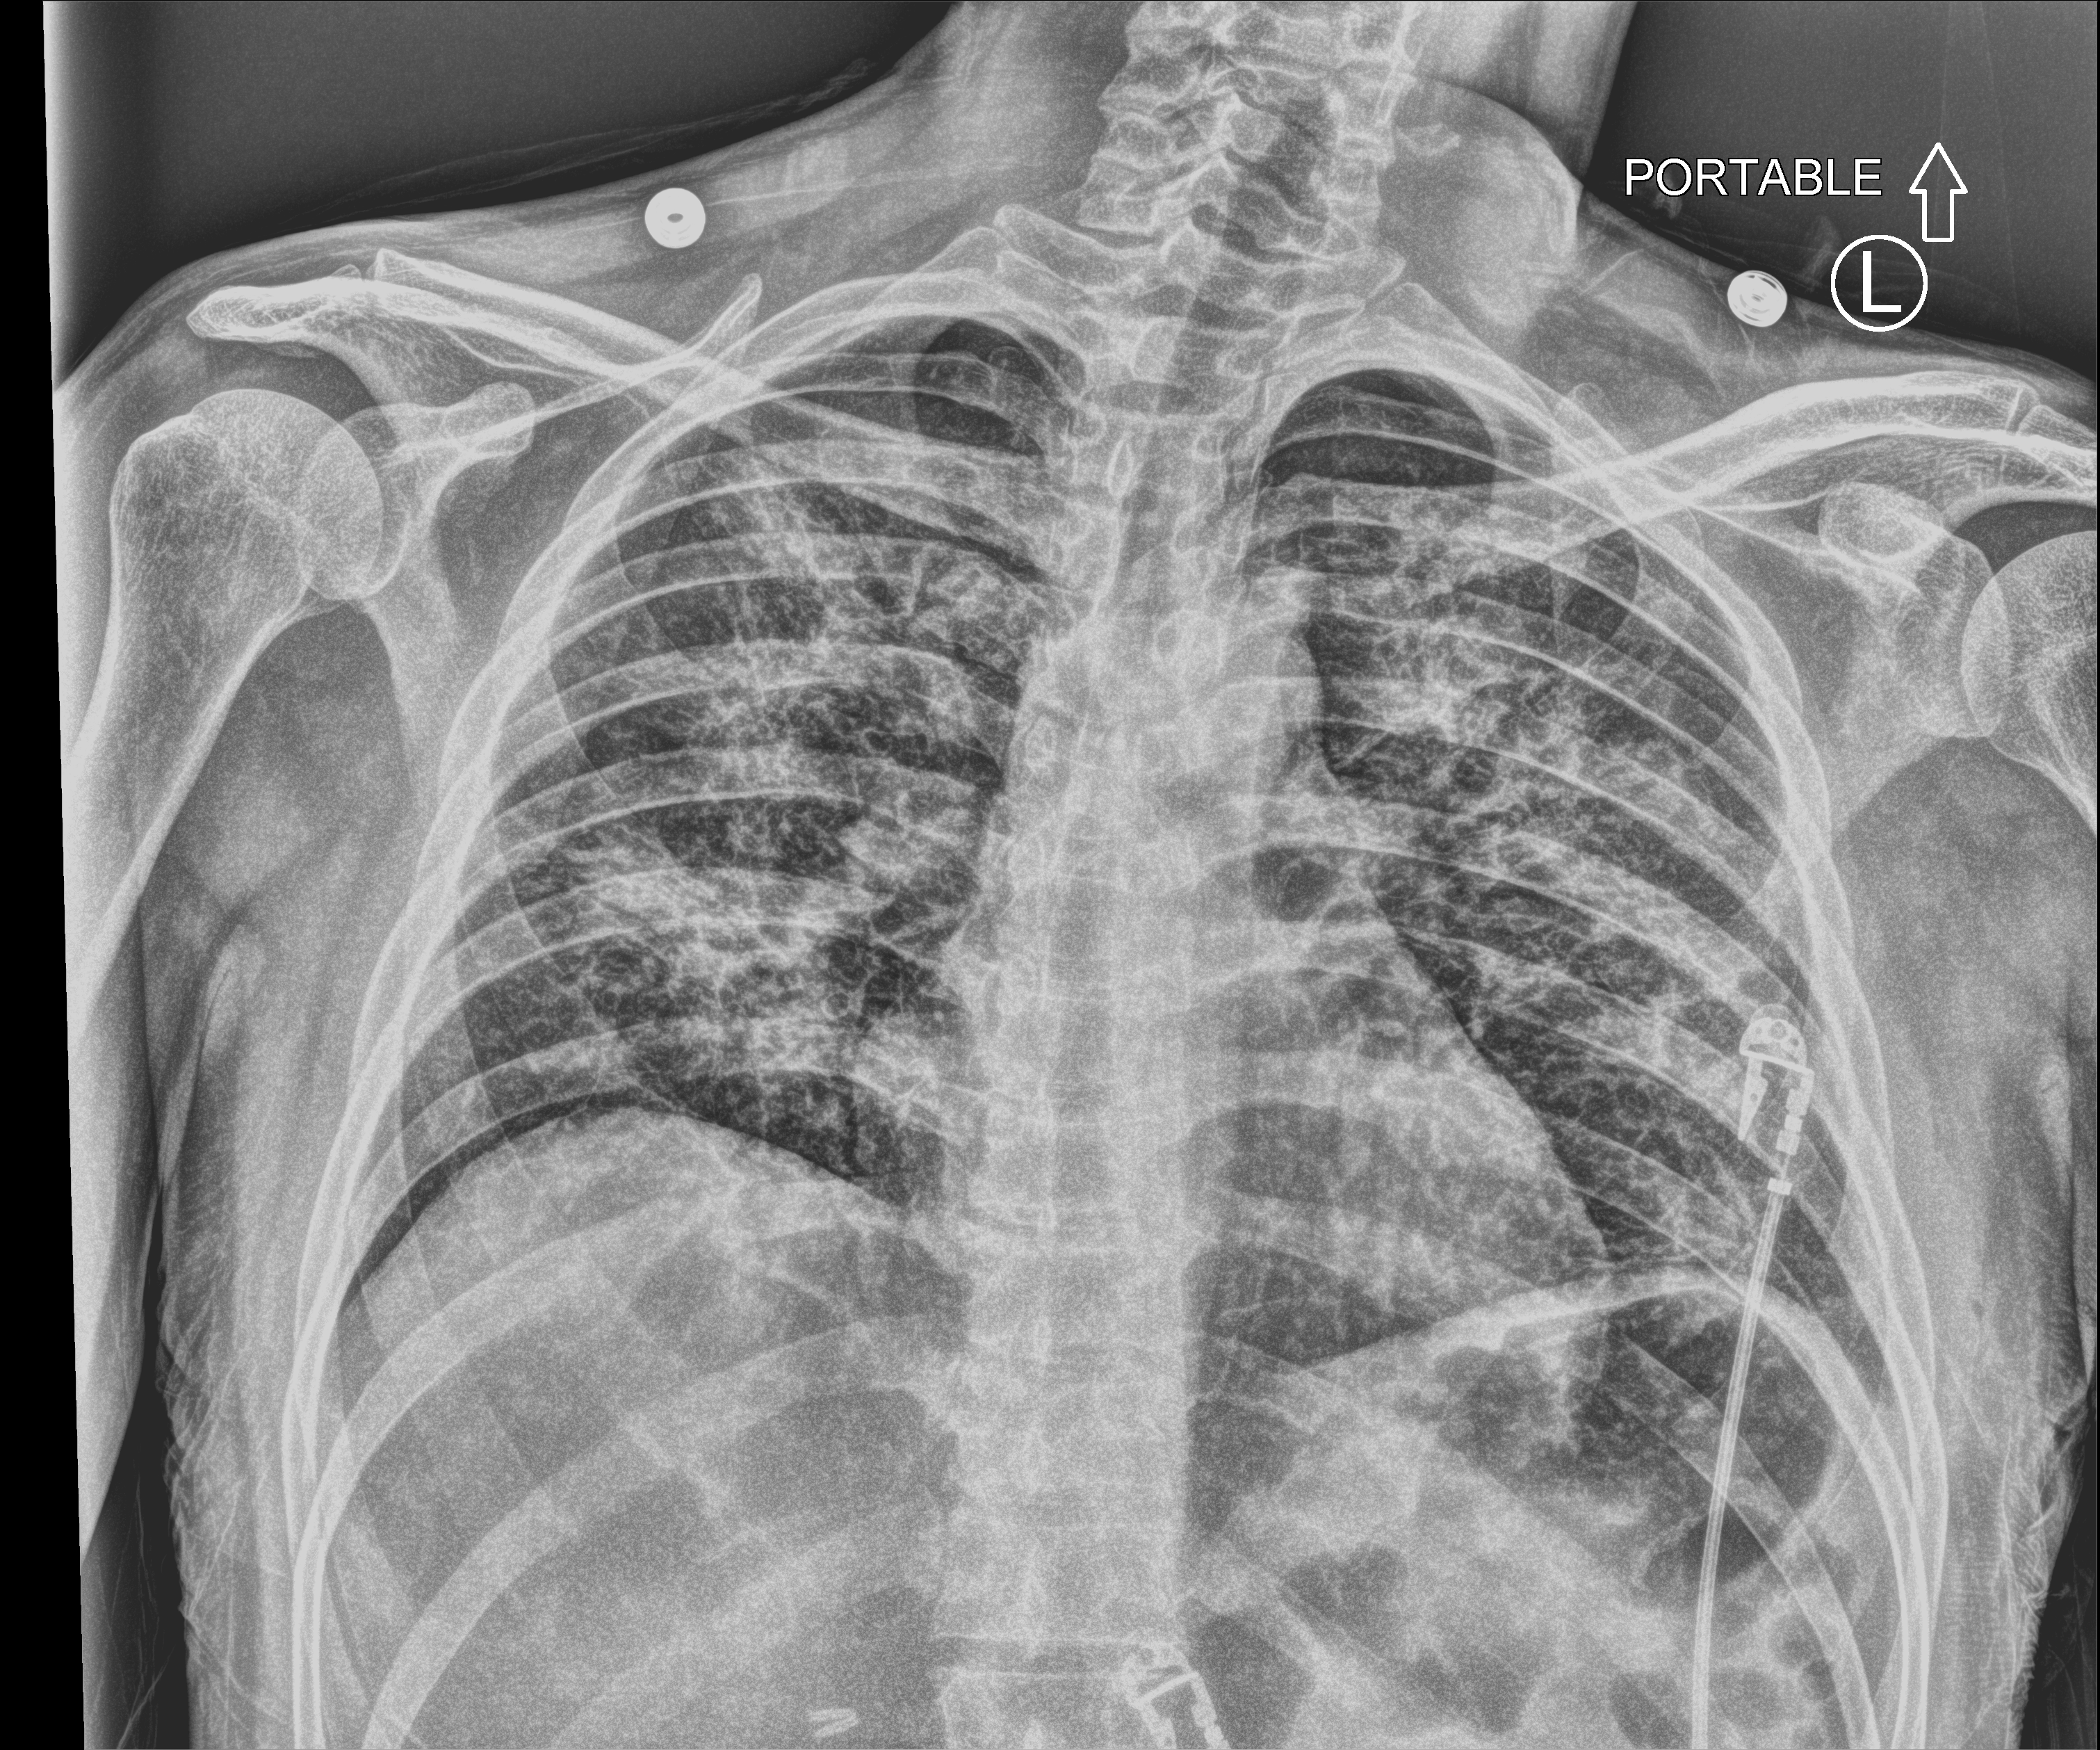
Portable chest radiograph. Male patient hospitalised with COVID-19, age 18–59 years.
Hospital-stay facts (about this admission, not read from this image; timing relative to this image not recorded):
- length of hospital stay: 29 days